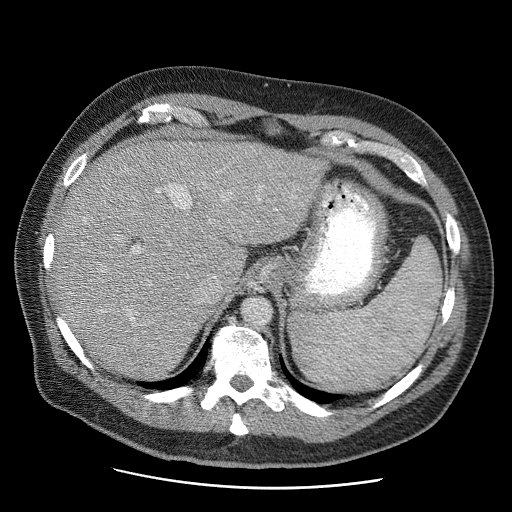
Contrast-enhanced abdominal CT (liver protocol), one axial slice; slice 41 of 81 in the series (ordered by position); reconstruction kernel STANDARD; 120 kVp; soft-tissue window (W 400 / L 40 HU); 2.5 mm slice thickness; 512 × 512 image matrix. From the clinical record (not read from this slice): diagnosis: hepatocellular carcinoma (patient treated with transarterial chemoembolisation; whether this scan precedes or follows treatment is not stated here); TNM stage (as recorded): Stage-IIIA; Child-Pugh class: A; tumour differentiation: moderately differentiated; tumour size: 5.5 cm.
Outlined on this slice (semi-automatically segmented with operator editing):
- liver parenchyma outside the tumour (the mass and vessels are separate outlines, so this box may not span the whole liver): box from (x=54, y=140) to (x=326, y=378) px
- liver vessels: (x=103, y=185)–(x=276, y=320)